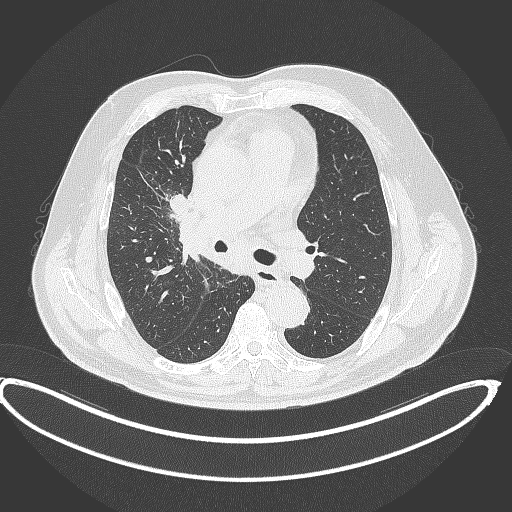
Chest CT, one axial slice; slice 246 of 390 in the series (ordered by position); lung window (W 1500 / L -600 HU); 1 mm slice thickness; 512 × 512 image matrix, field of view 448 × 448 mm. Male patient, age 62 years. Case-level facts recorded for this patient, not image findings: clinical TNM (as recorded): T1c N3 M1c.
Structures marked on this image (rectangle marked by the reading radiologist):
- lung tumour (recorded histology: adenocarcinoma): box from (x=164, y=188) to (x=193, y=216) px